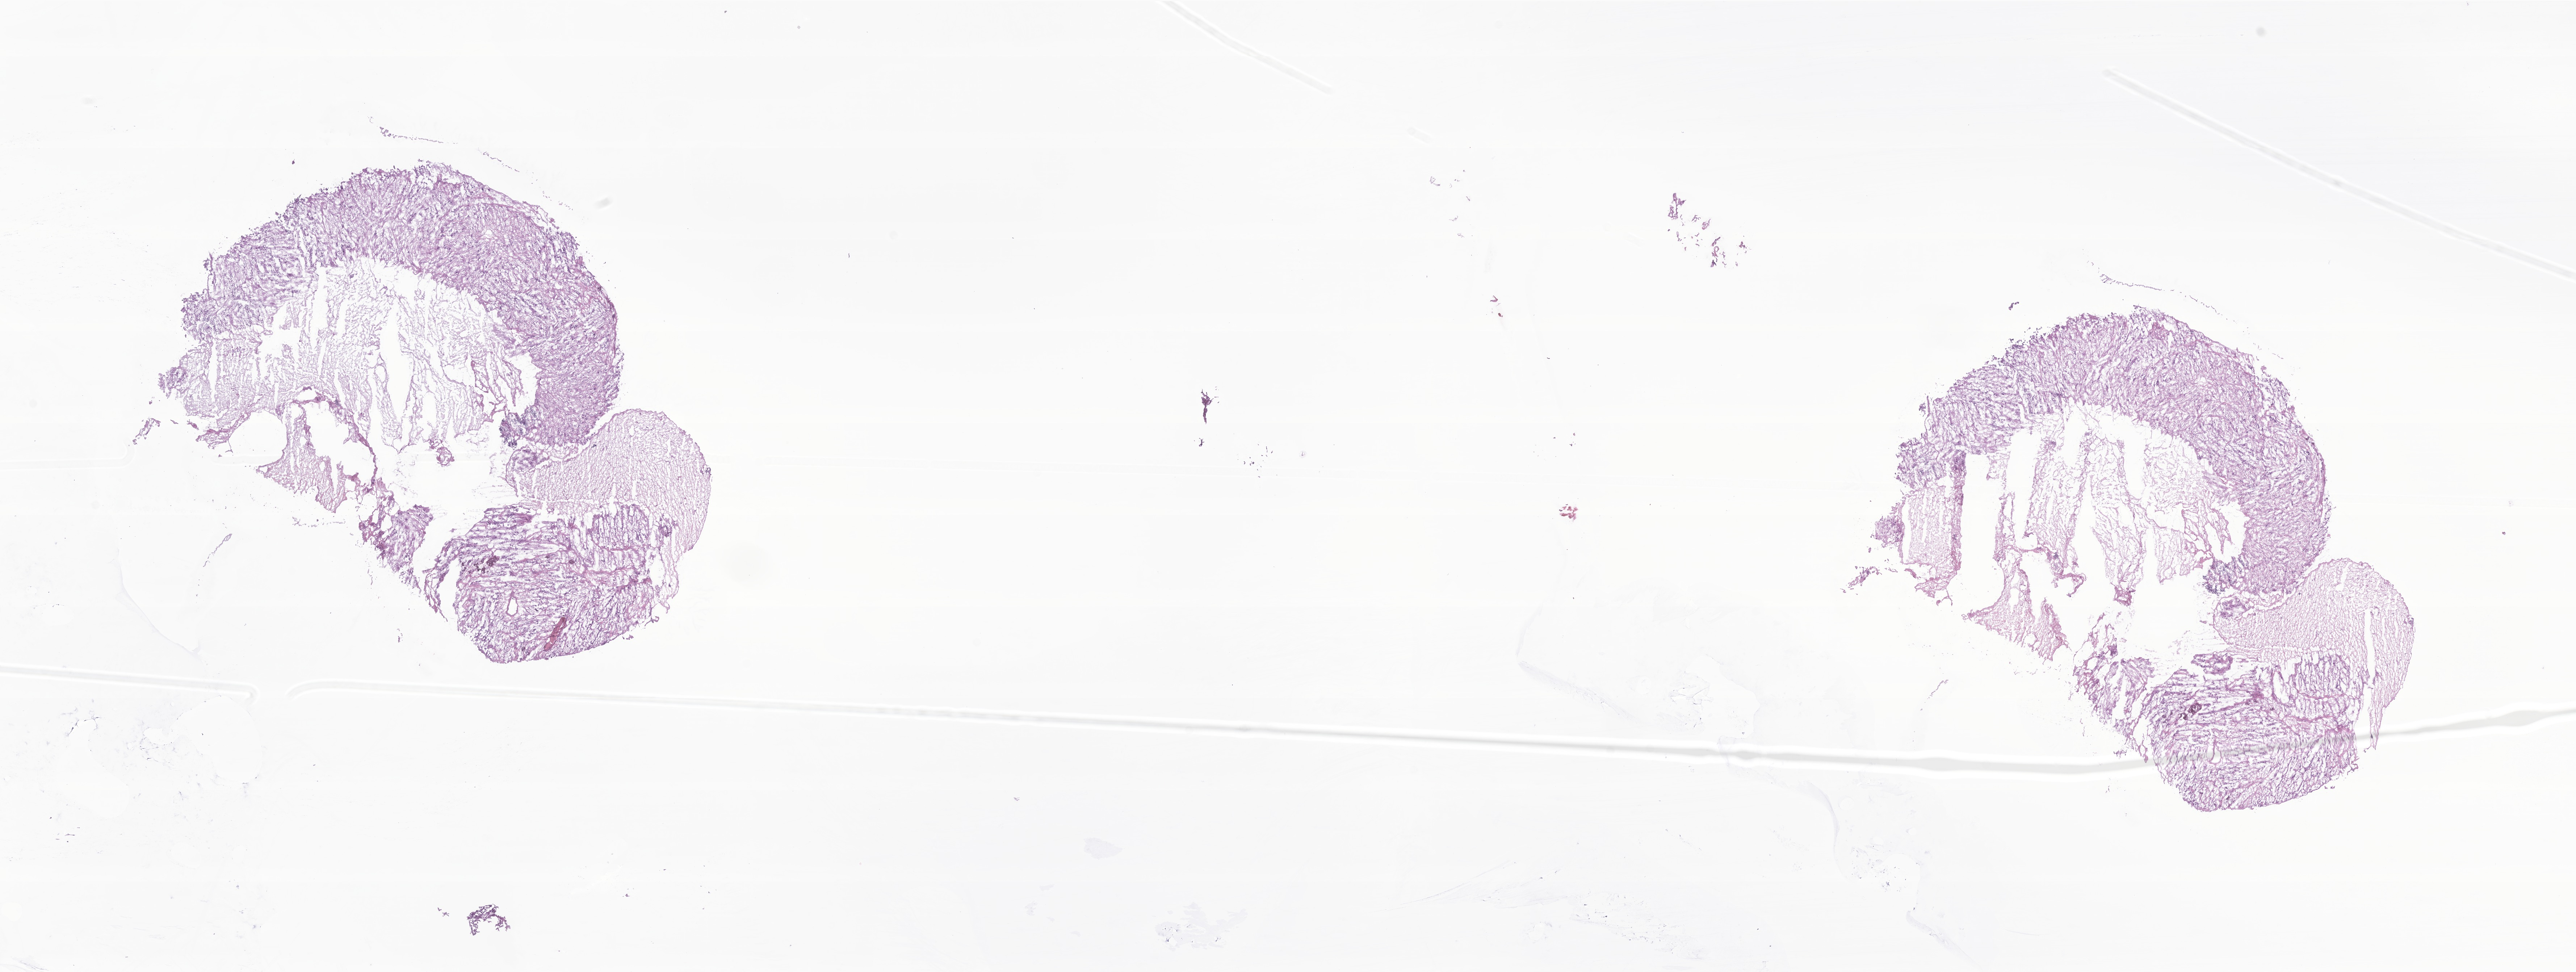
Haematoxylin and eosin whole-slide image of tumor tissue from the adrenal gland — whole scanned area (about 30.0 x 11.3 mm) shown as a low-resolution overview; cryosection (OCT / tissue freezing medium). Patient: female, age 749 days (about 2.1 years).
Diagnosis (ICD-O-3 morphology term): Ganglioneuroblastoma.